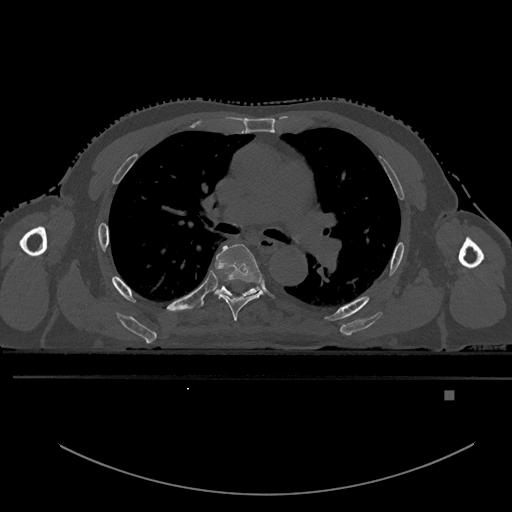
CT including the spine, one axial slice. Slice 341 of 969 in the series (ordered by position). Bone window (W 1800 / L 400 HU). 0.5 mm slice thickness. 512 × 512 image matrix, field of view 456 × 456 mm. Patient: male, 82 years. From the clinical record (not read from this slice): primary cancer: prostate.
Outlined on this slice (semi-automatically segmented with operator editing):
- T5 vertebra: box from (x=214, y=243) to (x=263, y=321) px
- T6 vertebra: (x=198, y=286)–(x=260, y=307)